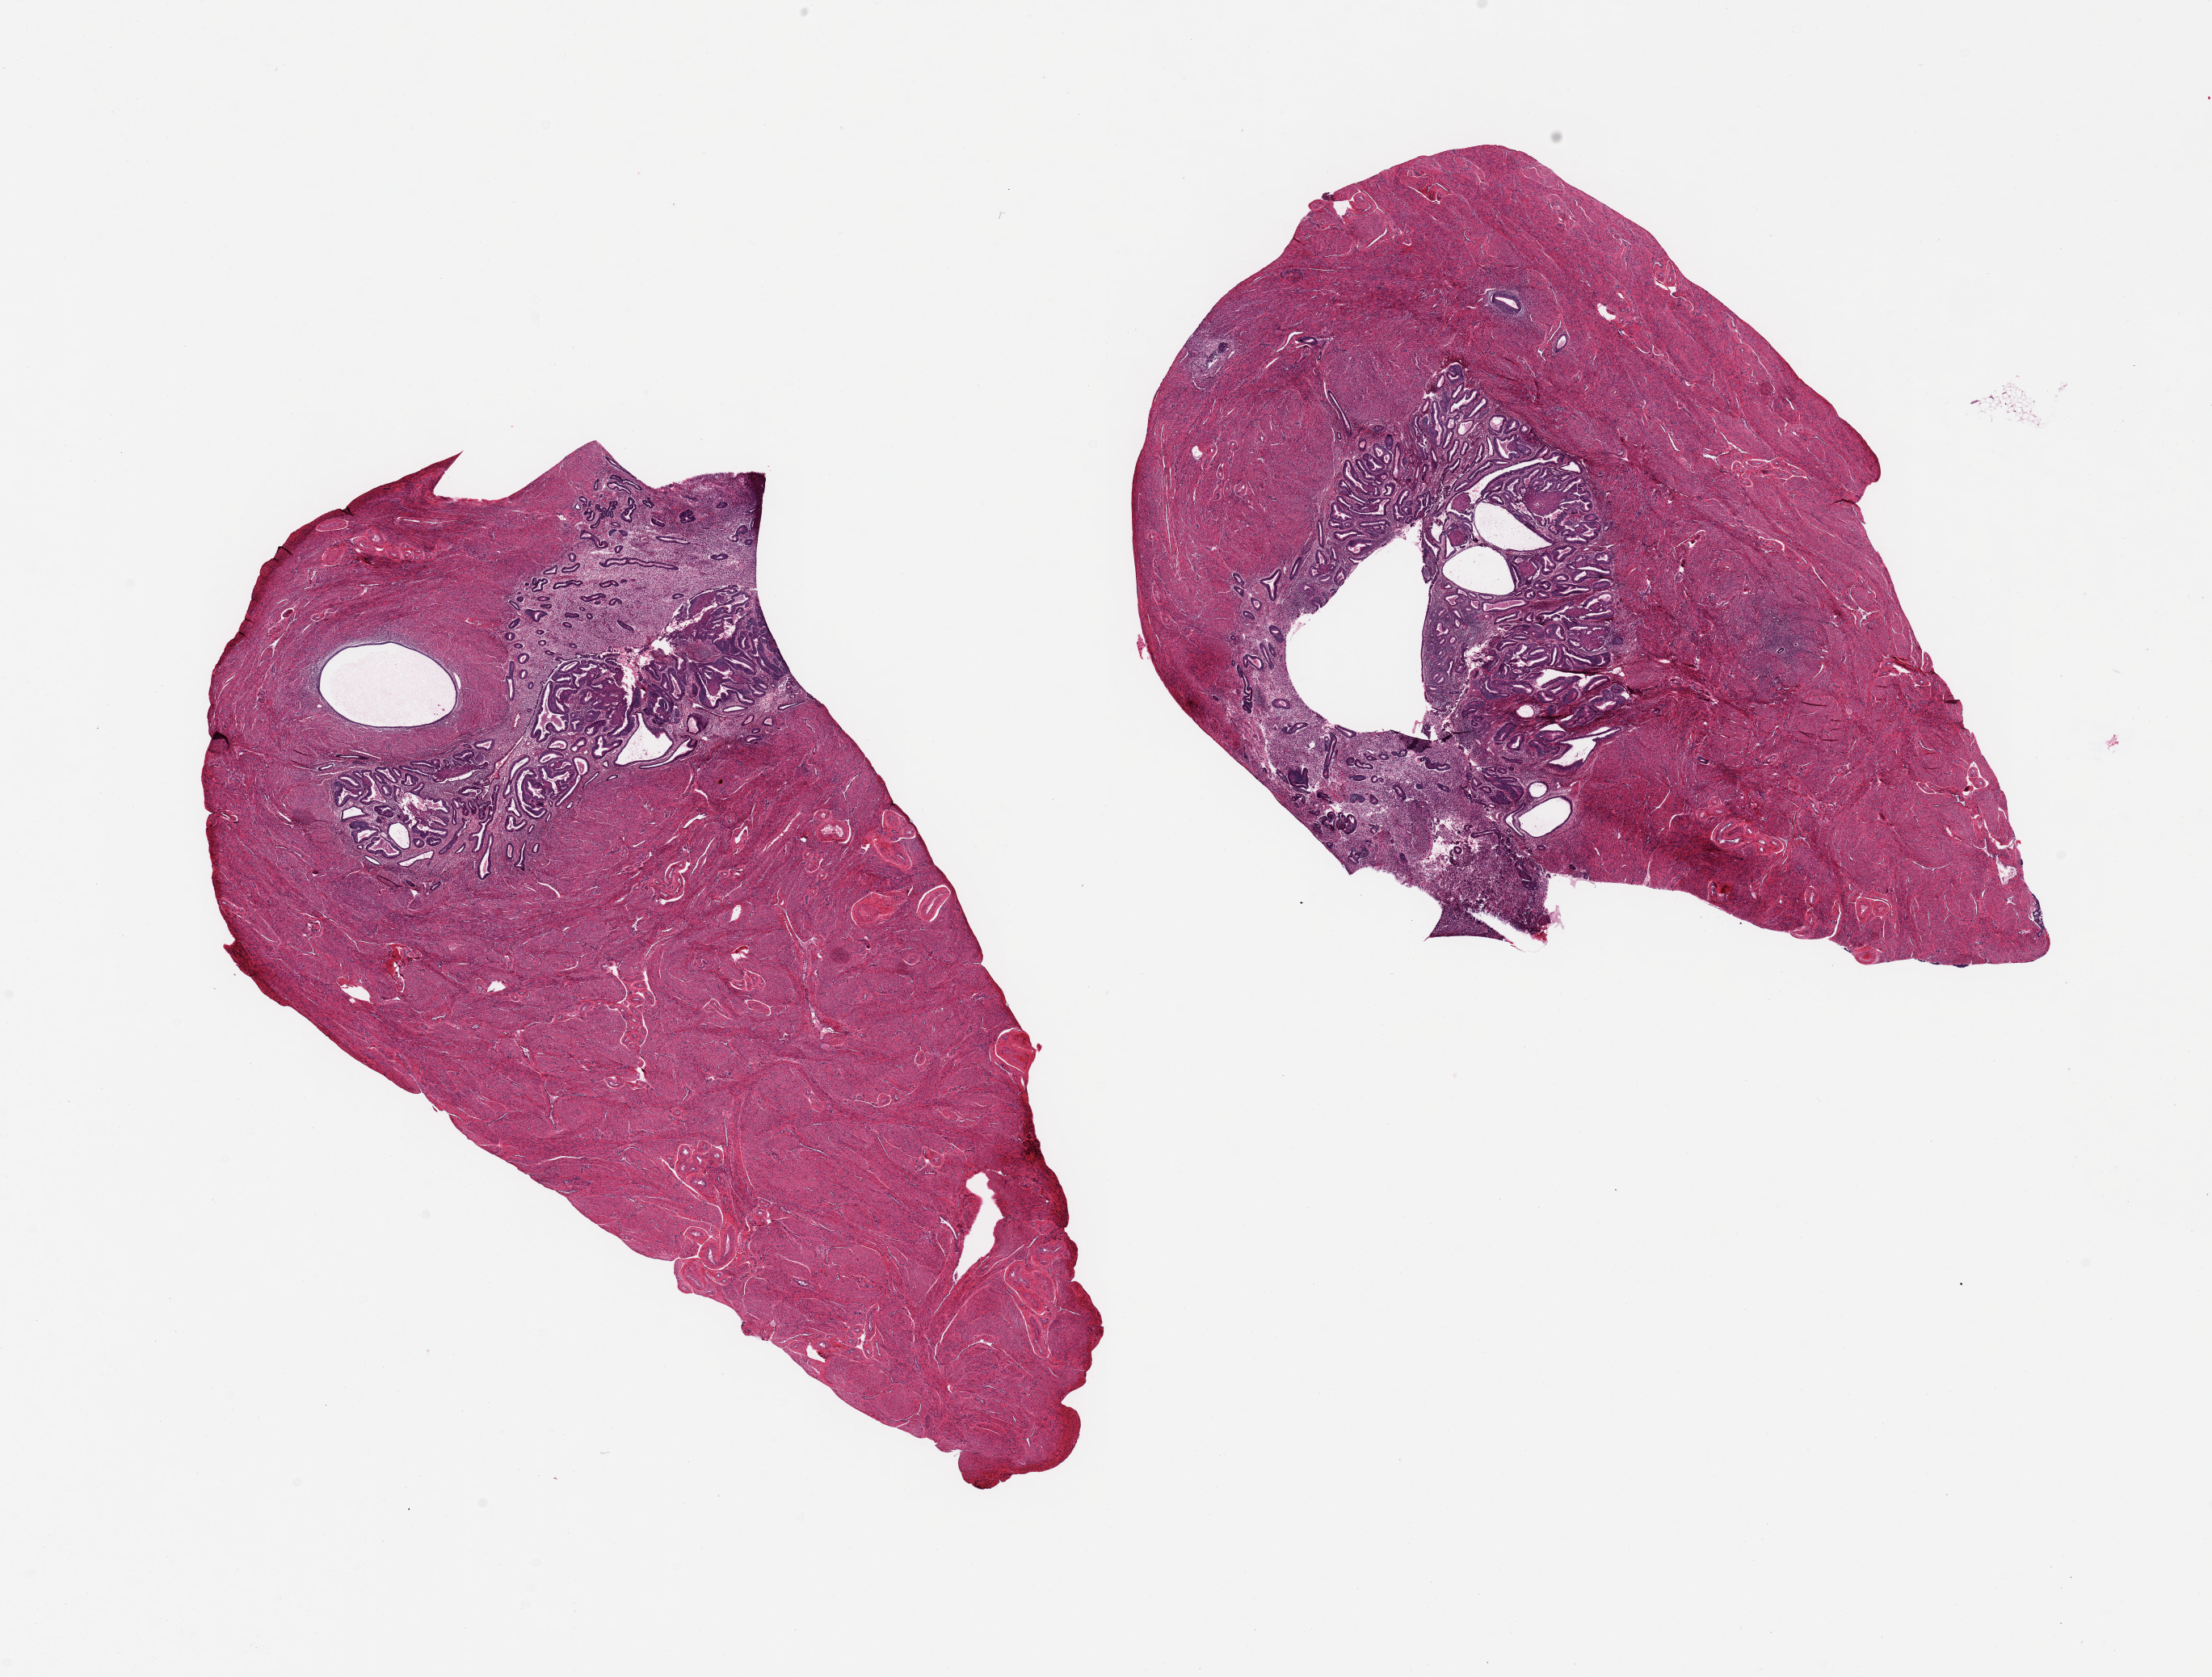
Hematoxylin and eosin (H&E) whole-slide image, brightfield — shown as a low-resolution overview of the whole scanned area (about 21.7 x 16.4 mm), PAXgene-fixed, paraffin-embedded tissue, section of uterus (target tissue), donor tissue sample. Donor: female.
* pathologist's review note for this sample: 2 pieces; proliferative endometrium 10%, with endometrial hyperplastic polyp, 30%; myometrium comprises 60%